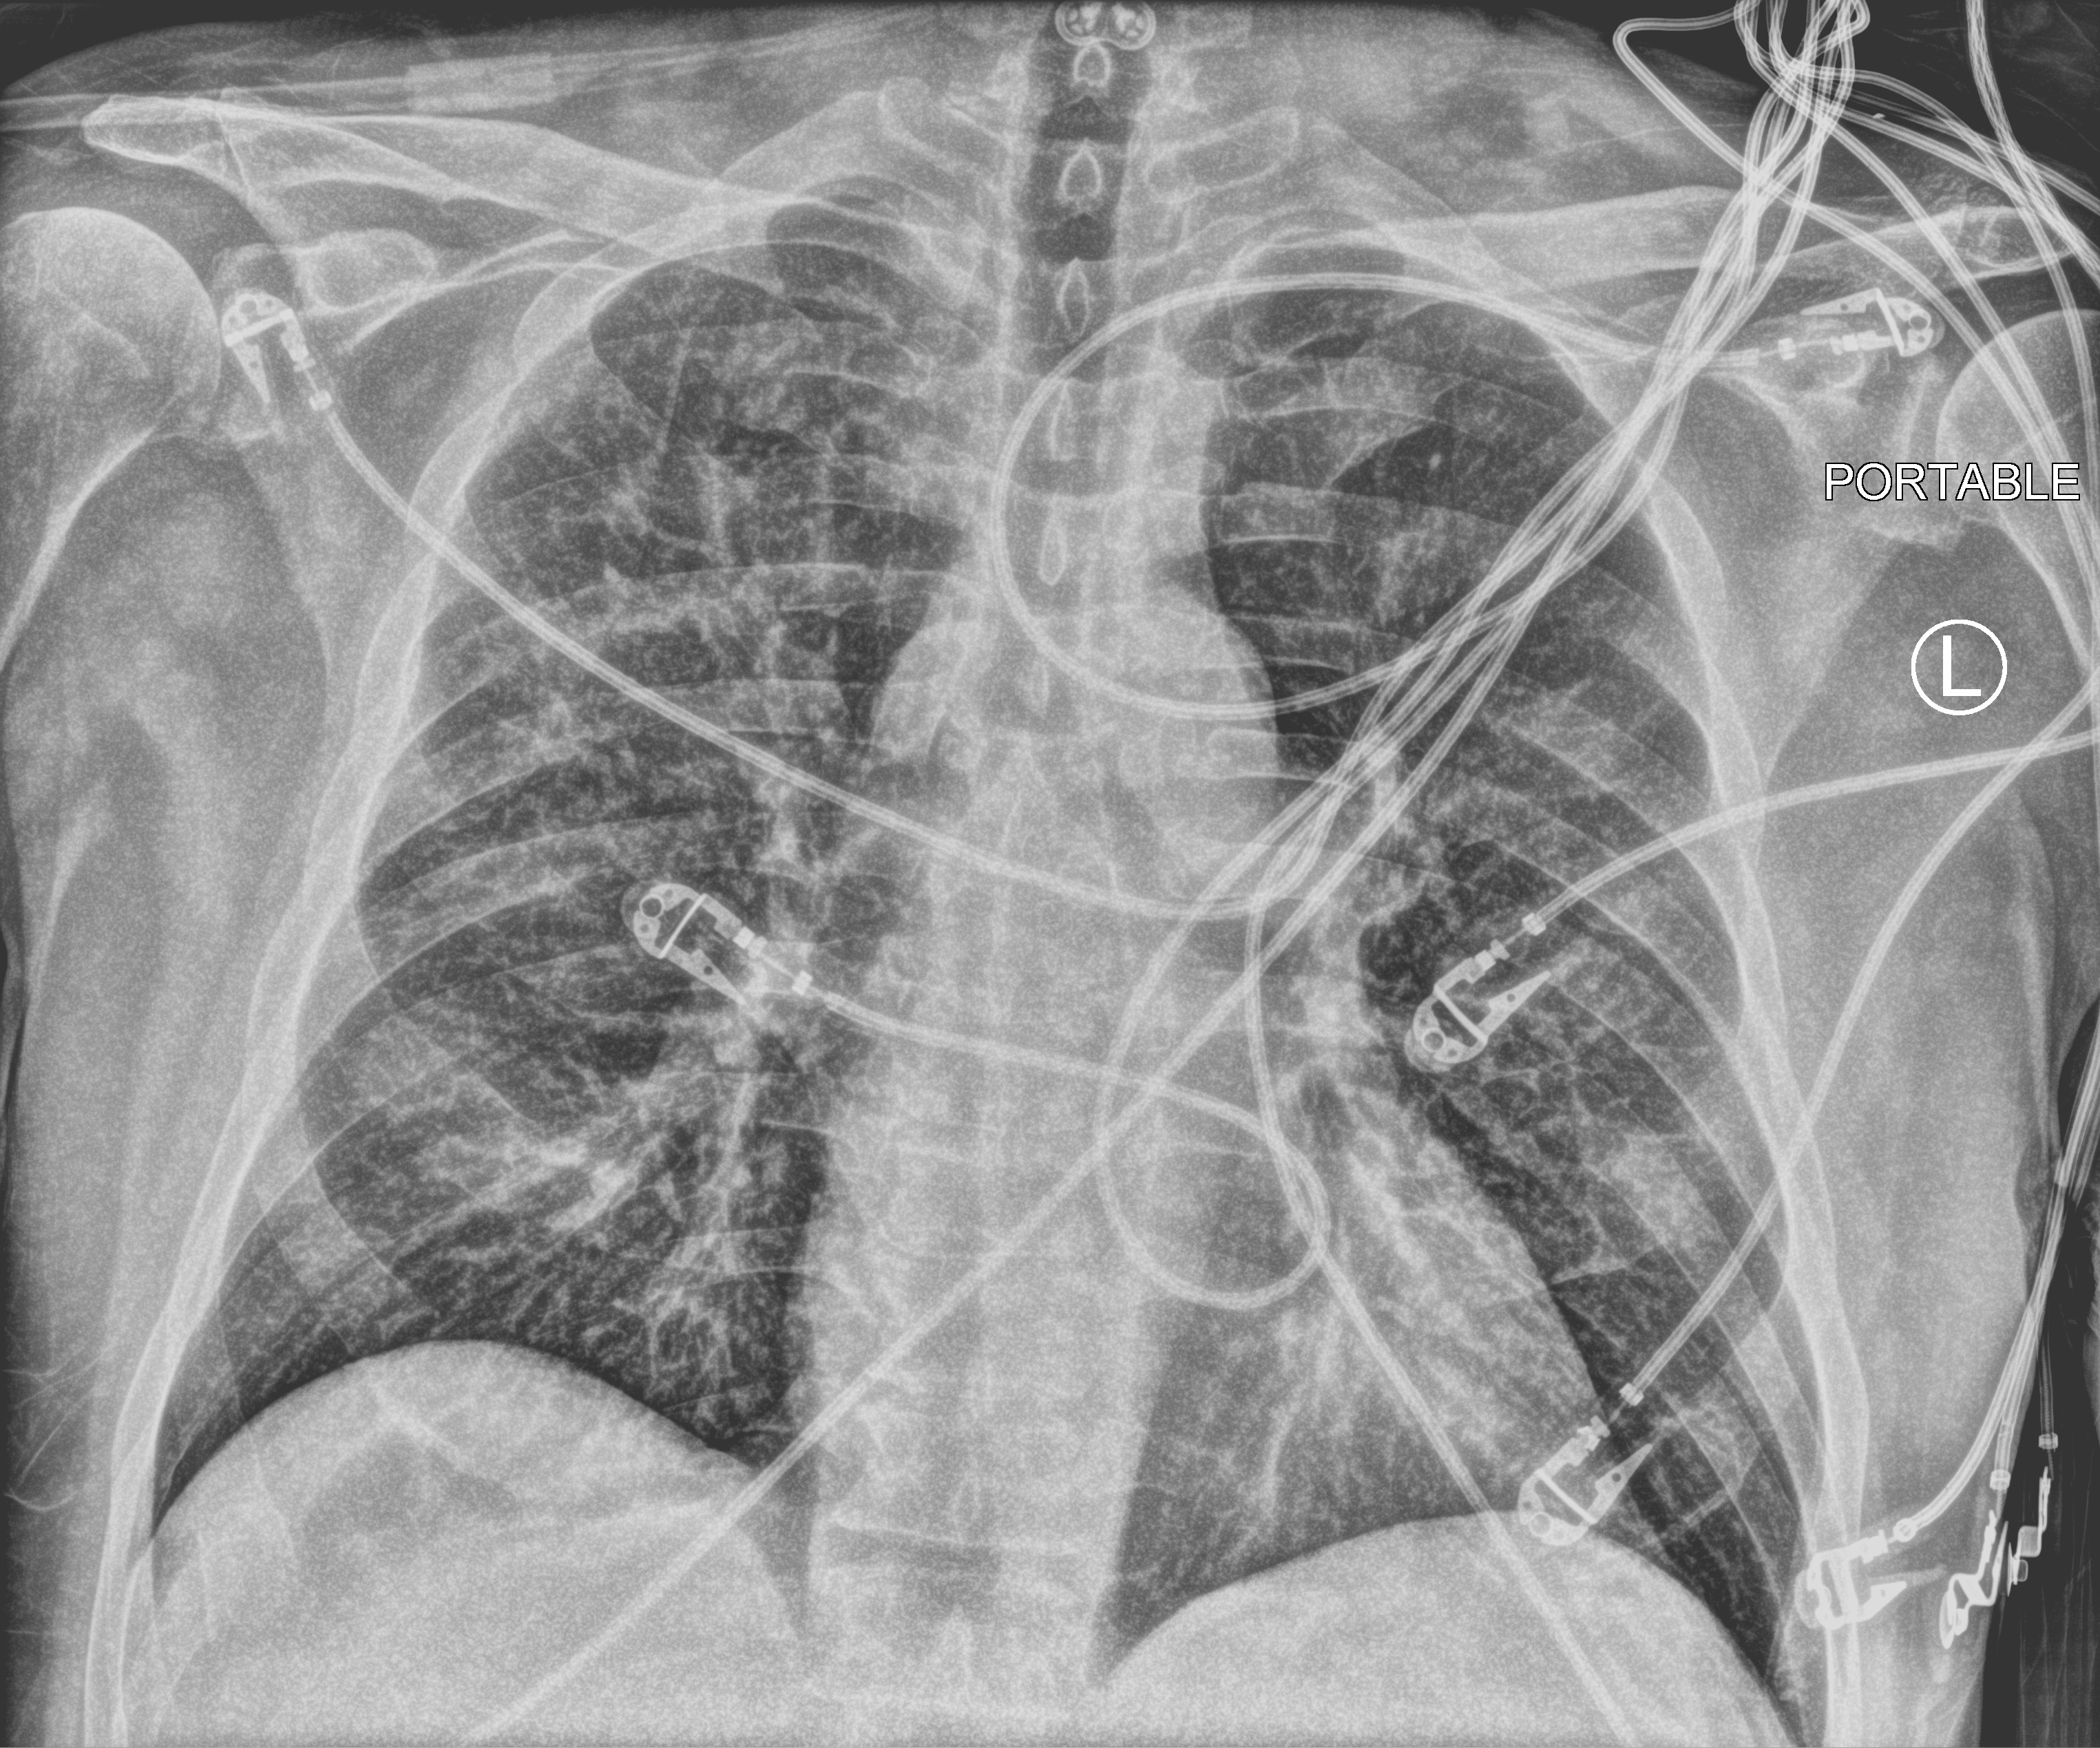
Chest X-ray (portable); anteroposterior (AP) projection. Male patient hospitalised with COVID-19, age 60–74 years.
Hospital-stay facts (about this admission, not read from this image; timing relative to this image not recorded): mechanically ventilated during this hospital stay: no.